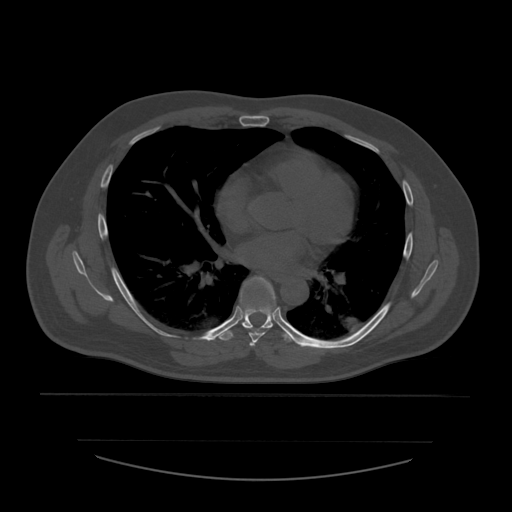
CT including the spine, one axial slice; slice 368 of 532 in the series (ordered by position); reconstruction kernel STANDARD; bone window (W 1800 / L 400 HU); 1.25 mm slice thickness; 512 × 512 image matrix. Patient age 44 years. Case-level facts recorded for this patient, not image findings: primary cancer: soft tissue sarcoma.
Annotated regions visible in this slice (semi-automatic segmentation, software-assisted and operator-edited):
- T5 vertebra: bounding box <250,342,254,346> (left, top, right, bottom; pixels)
- T6 vertebra: <240,277,276,346>
- T7 vertebra: <217,281,293,342>